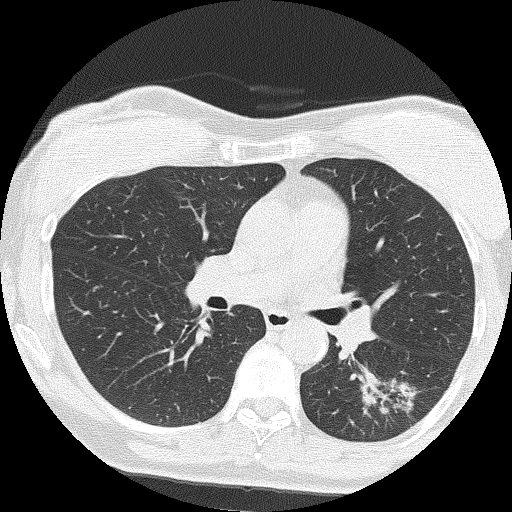
Low-dose screening chest CT, axial slice; second annual screen; lung window (W 1500 / L -600 HU); 2 mm slice thickness; 120 kVp; 512 × 512 image matrix. Female participant, aged 64 years at enrolment. Former smoker at enrolment.
- Lesion marked by an expert reader, bounding box [x1, y1, x2, y2] px = [358, 366, 441, 438].
- The screening reader recorded 3 non-calcified nodules or masses ≥4 mm on this exam; which of them this box marks is not recorded.
- Official screen result: positive, other.
- Lung cancer was diagnosed 576 days after this screen (after the third annual screen): adenocarcinoma, NOS, left lower lobe, moderately differentiated (G2), stage IA (AJCC 6th edition), 17 mm at pathology.